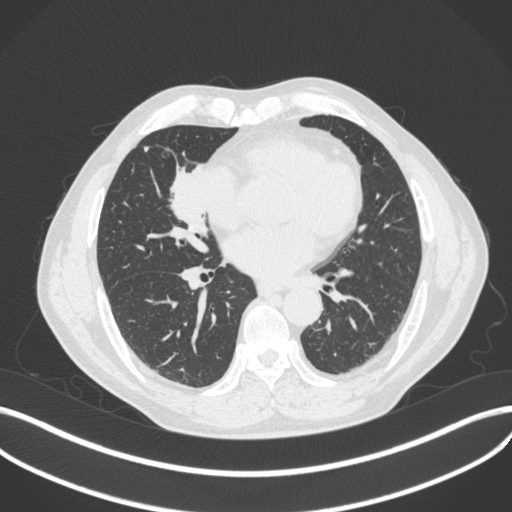
Chest CT, one axial slice; reconstruction kernel B31f; lung window (W 1500 / L -600 HU); 512 × 512 image matrix, field of view 400 × 400 mm. Patient: male, 61 years. Case-level facts recorded for this patient, not image findings: clinical TNM (as recorded): T2b N1 M0.
Outlined on this slice (rectangle marked by the reading radiologist):
- lung tumour (recorded histology: squamous cell carcinoma): bounding box [x1, y1, x2, y2] px = [163, 150, 210, 242]